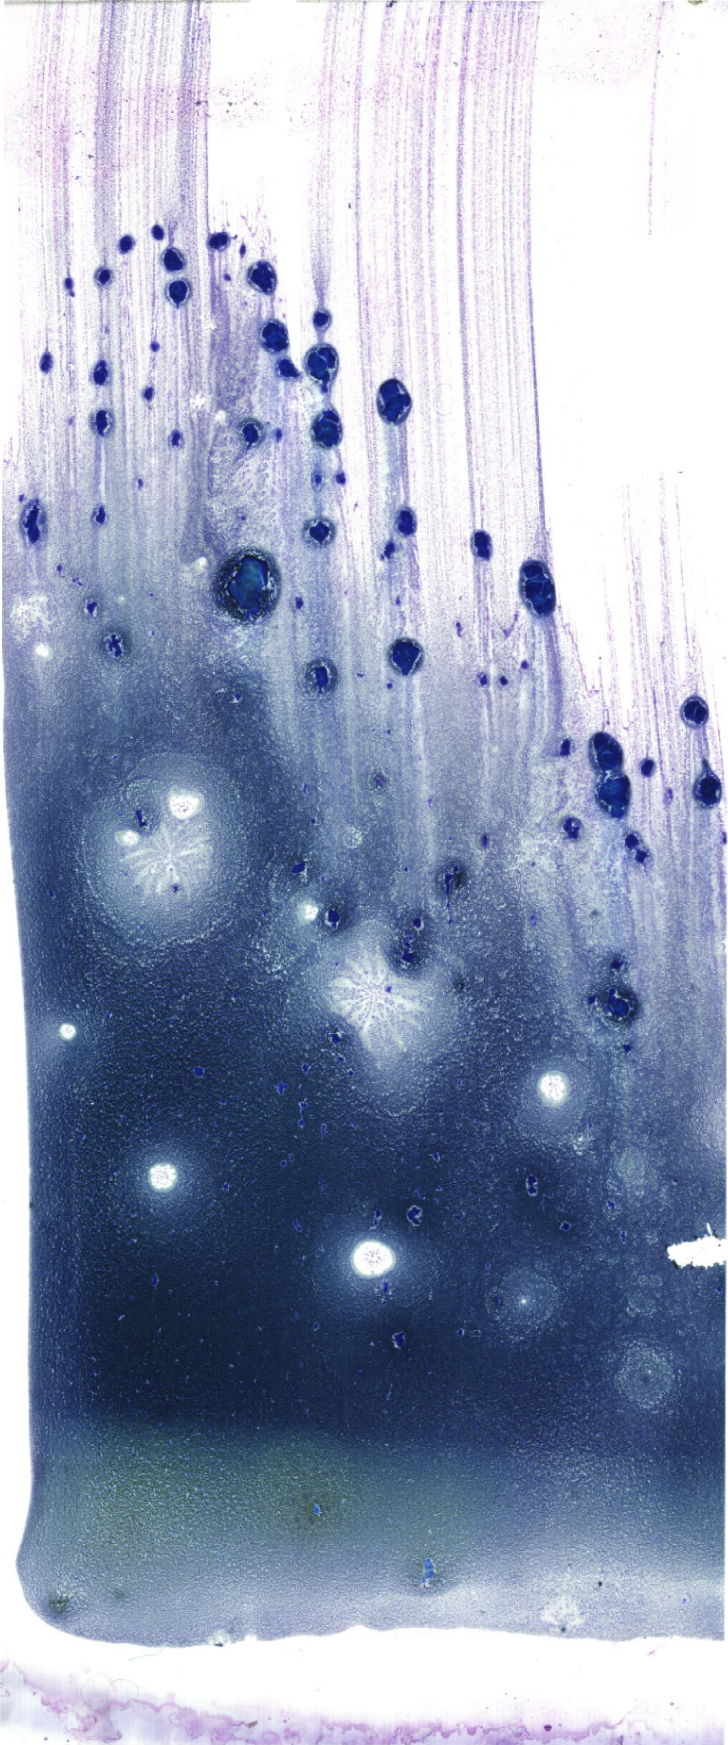
May-Grünwald–Giemsa-stained marrow aspirate smear (whole slide) — a low-resolution overview of the entire scanned area, about 20.6 x 49.5 mm. Patient sex: female.
Diagnosis: Mixed Phenotype Acute Leukemia, B/Myeloid.